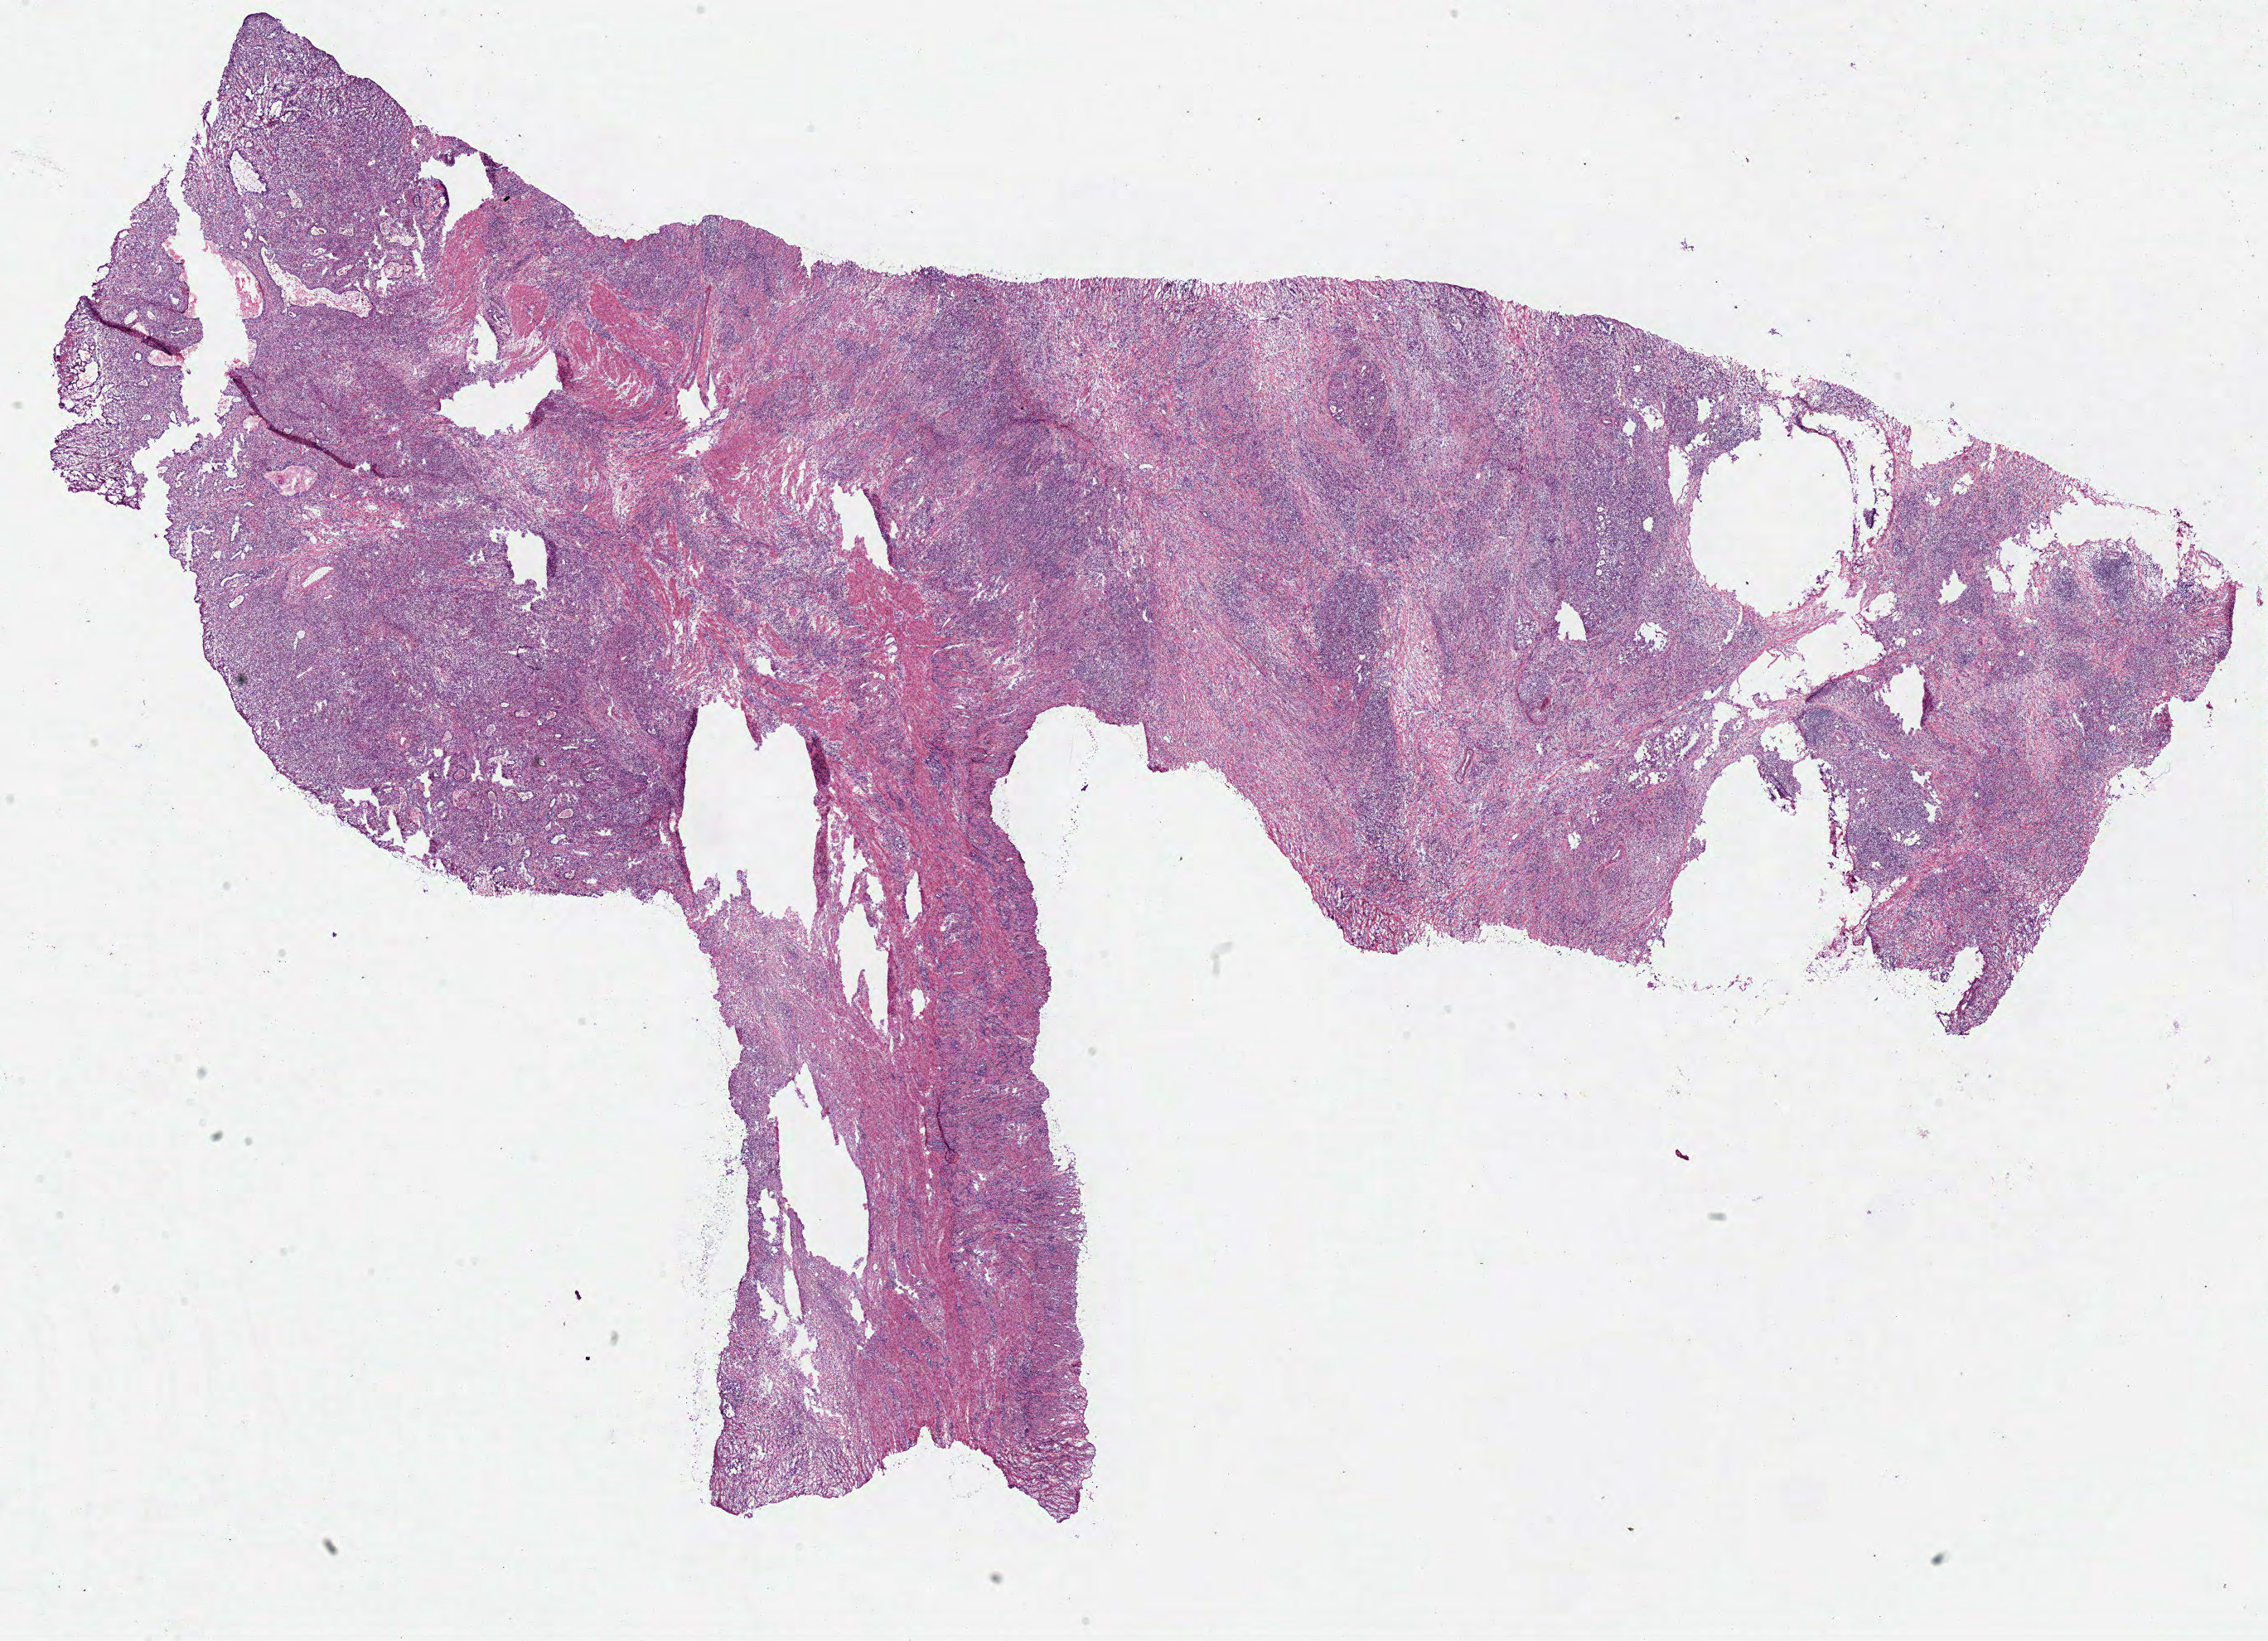
Hematoxylin and eosin (H&E) stained whole-slide image, a low-resolution overview of the entire scanned area, about 21.6 x 15.6 mm (from a 40x scan), frozen section from the bottom of the tissue portion, primary tumour sample from the stomach. Male, age 63 years at initial diagnosis. Histologic grade: G3 (poorly differentiated). Pathologist review of this section (percent, as recorded): tumour cells 80%, tumour nuclei 75%, normal cells 0%, stromal cells 15%, necrosis 5%.
• diagnosis: Adenocarcinoma, NOS (cardia, NOS)
• lymph nodes positive (case pathology): 5 of 15 examined
• AJCC pathologic stage: IIIA
• TNM: T3 N1 M0